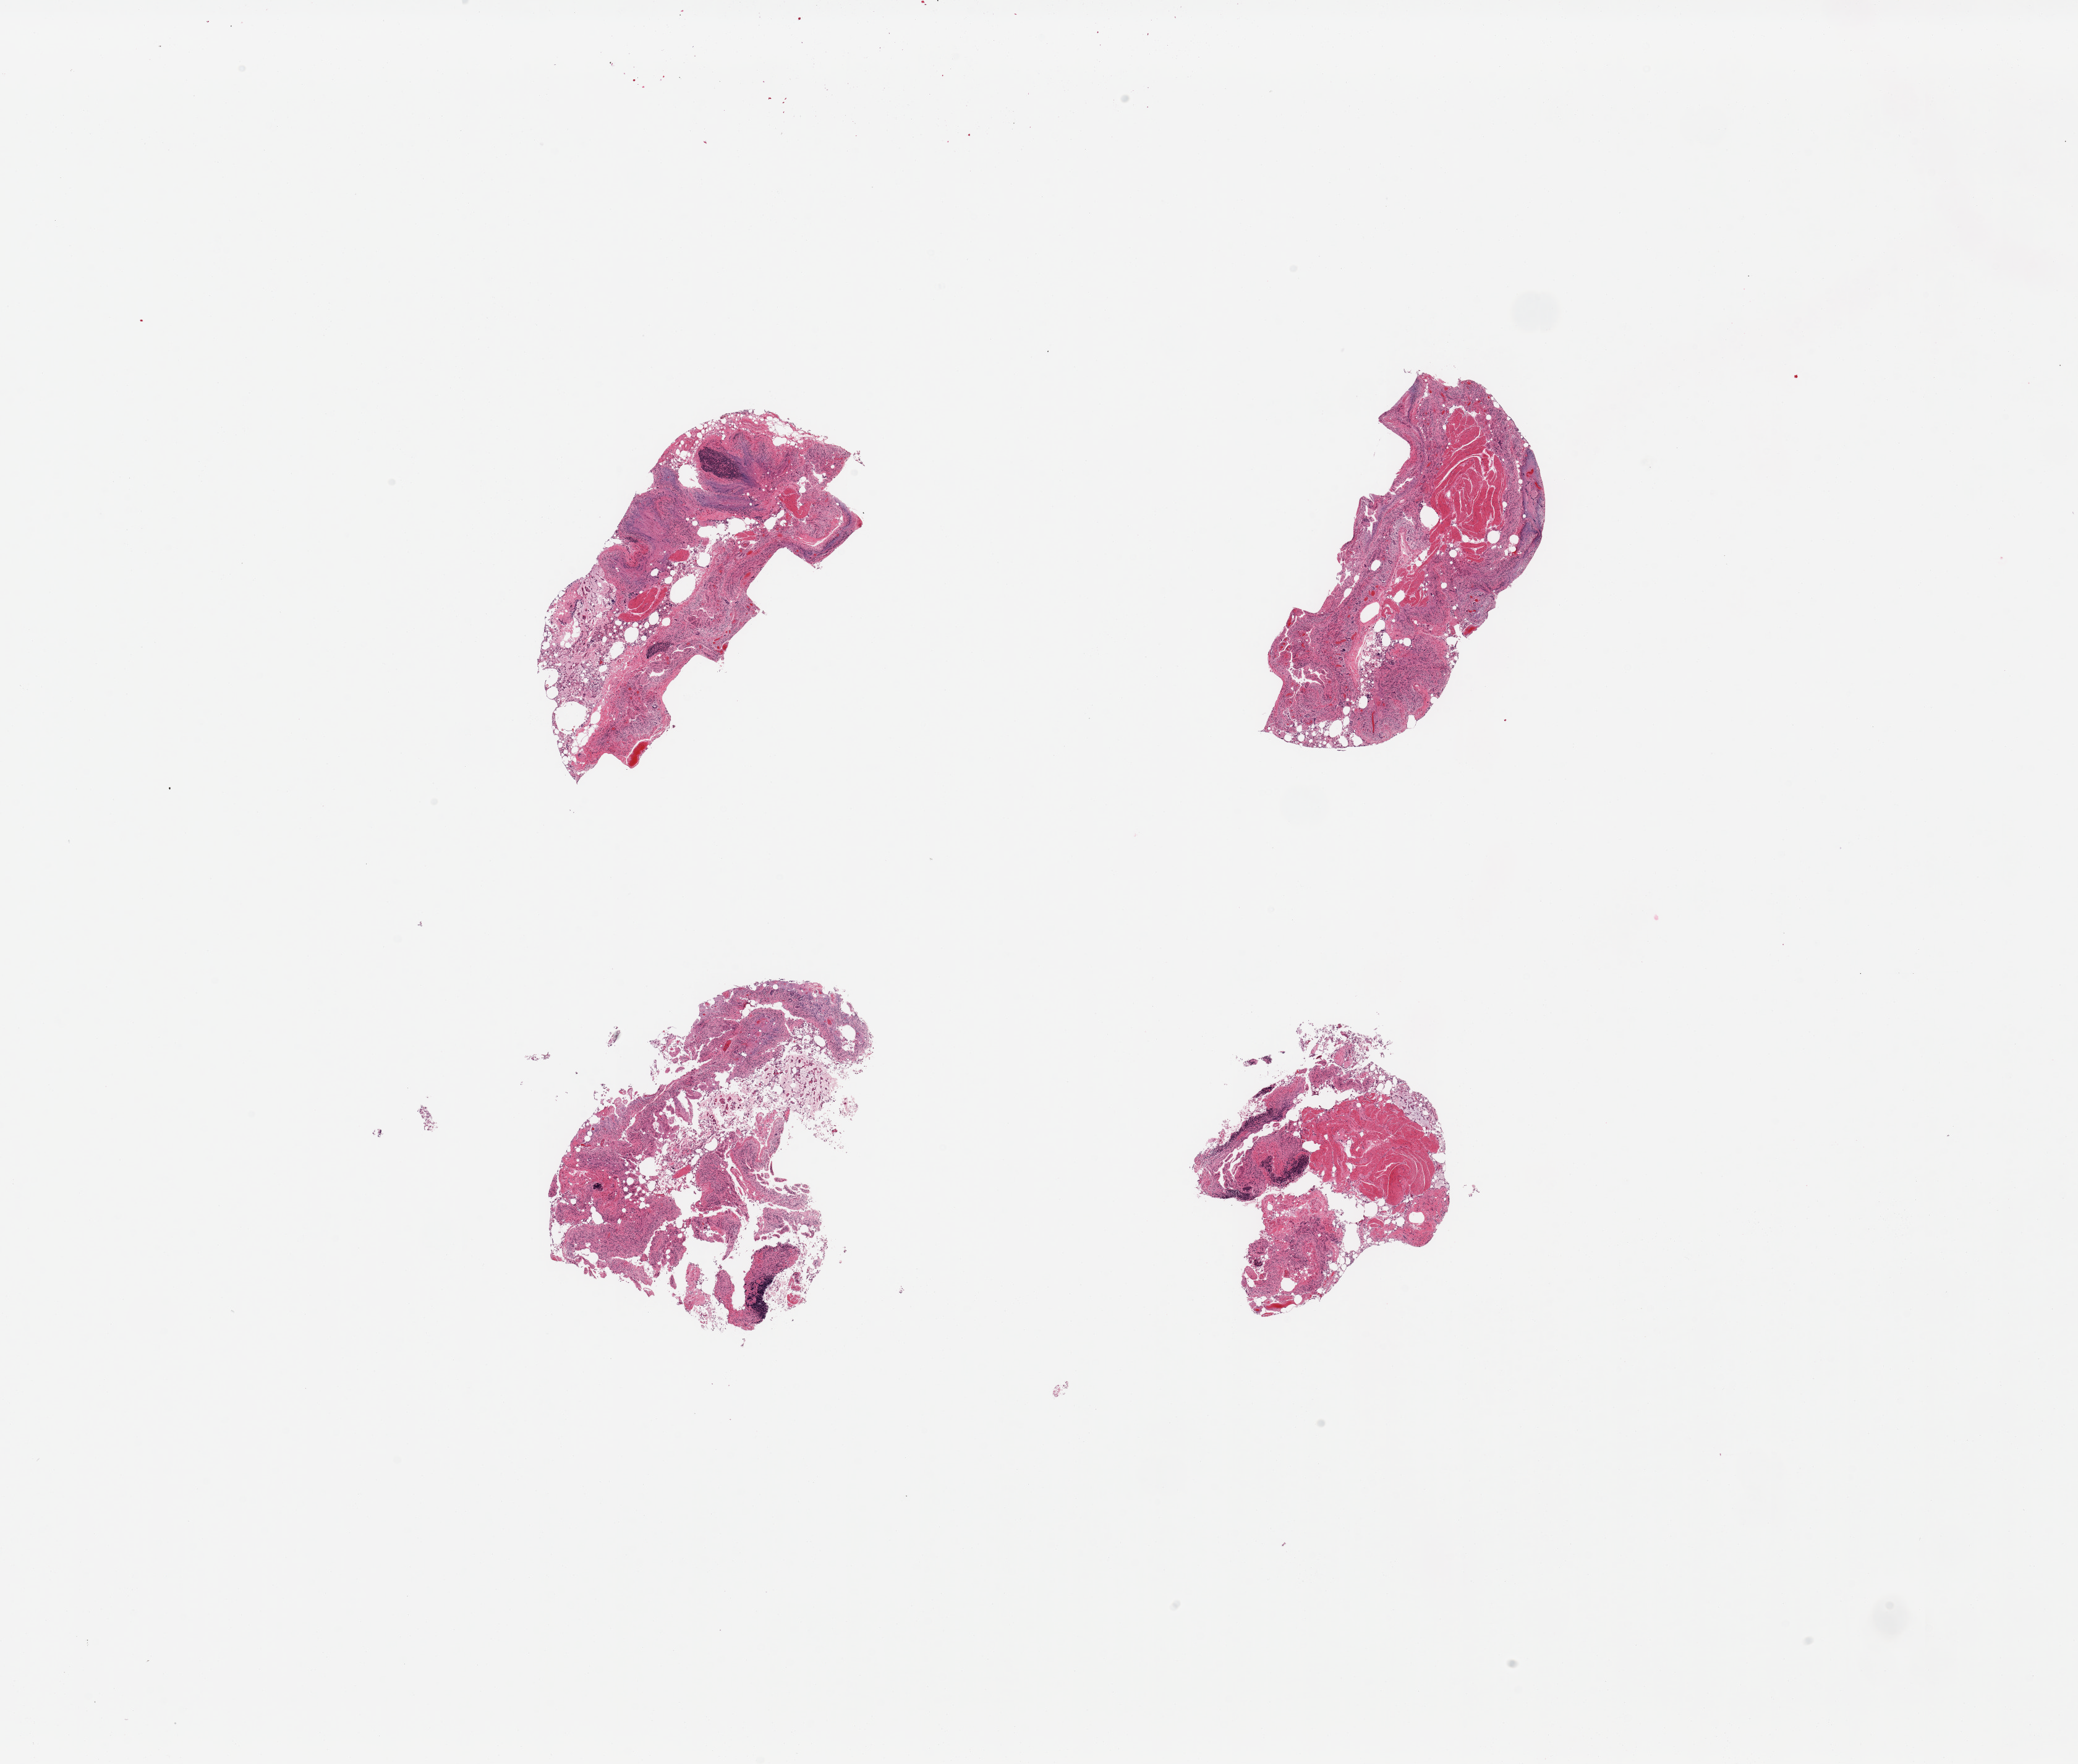
Whole-slide image, hematoxylin and eosin (H&E) stain, brightfield, low-resolution overview of the scanned area, about 26.6 x 22.6 mm. PAXgene-fixed, paraffin-embedded tissue. Section of ileum (target tissue). Donor tissue sample. Male donor.
• review note (as recorded): 4 pieces, advanced autolysis; correct site but insufficient target lymphoid aggregates (<5%)